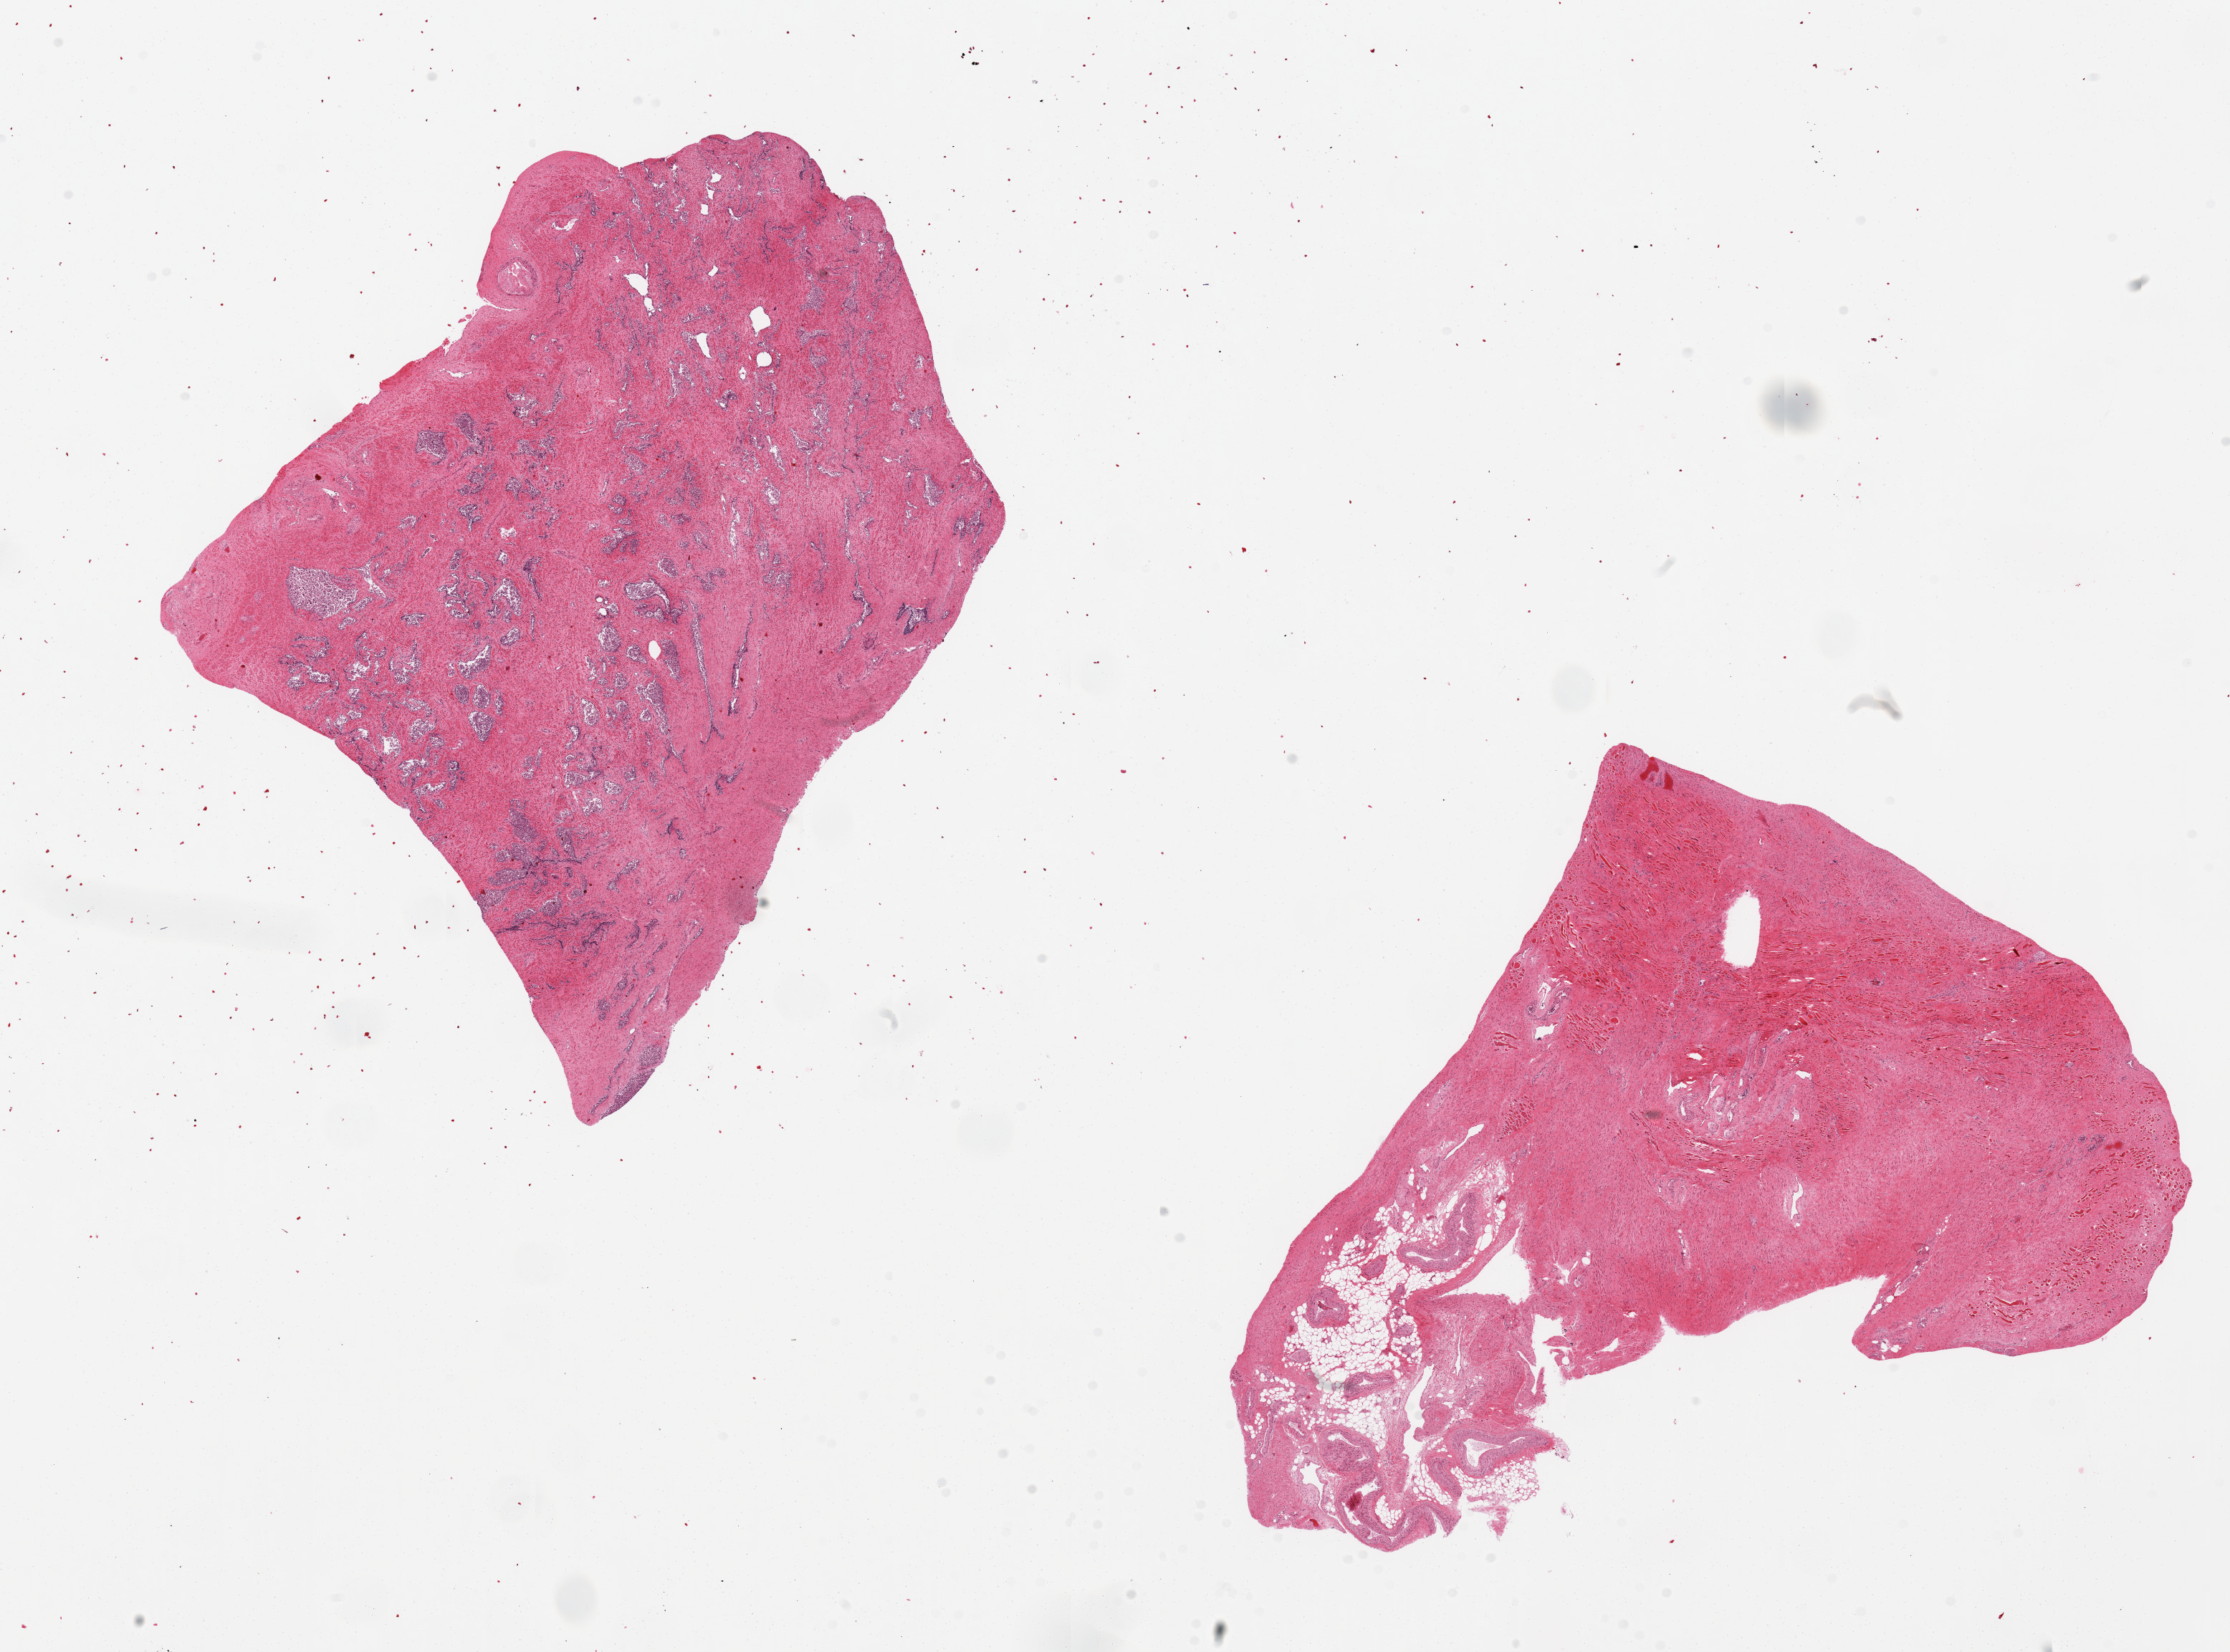
Whole-slide image, H&E stain, whole scanned area (about 24.6 x 18.2 mm) shown as a low-resolution overview; PAXgene-fixed paraffin-embedded (PFPE) section; sampled site (target tissue): prostate; tissue donor sample. Donor: male.
- review note (as recorded): 2 pieces; glands = 3; 1 piece is all stroma